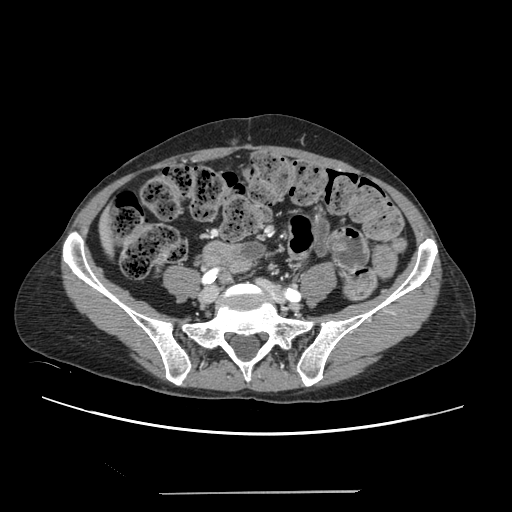
Contrast-enhanced abdominal CT, one axial slice. Position 9 of 240 along the scan axis. 120 kVp. Intravenous contrast given. Soft-tissue window (W 400 / L 40 HU). 1.25 mm slice thickness. 512 × 512 image matrix. Female patient, age 60 years. Case-level facts recorded for this patient, not image findings: diagnosis: colorectal cancer liver metastases, imaged before liver resection; multiple liver metastases: no; largest metastasis: 1.5 cm; disease in both lobes: no.
Structures marked on this image (manually delineated by an expert):
- liver: bounding box <103,230,109,246> (left, top, right, bottom; pixels)
- planned liver remnant (the part of the liver to remain after resection): <103,225,108,246>